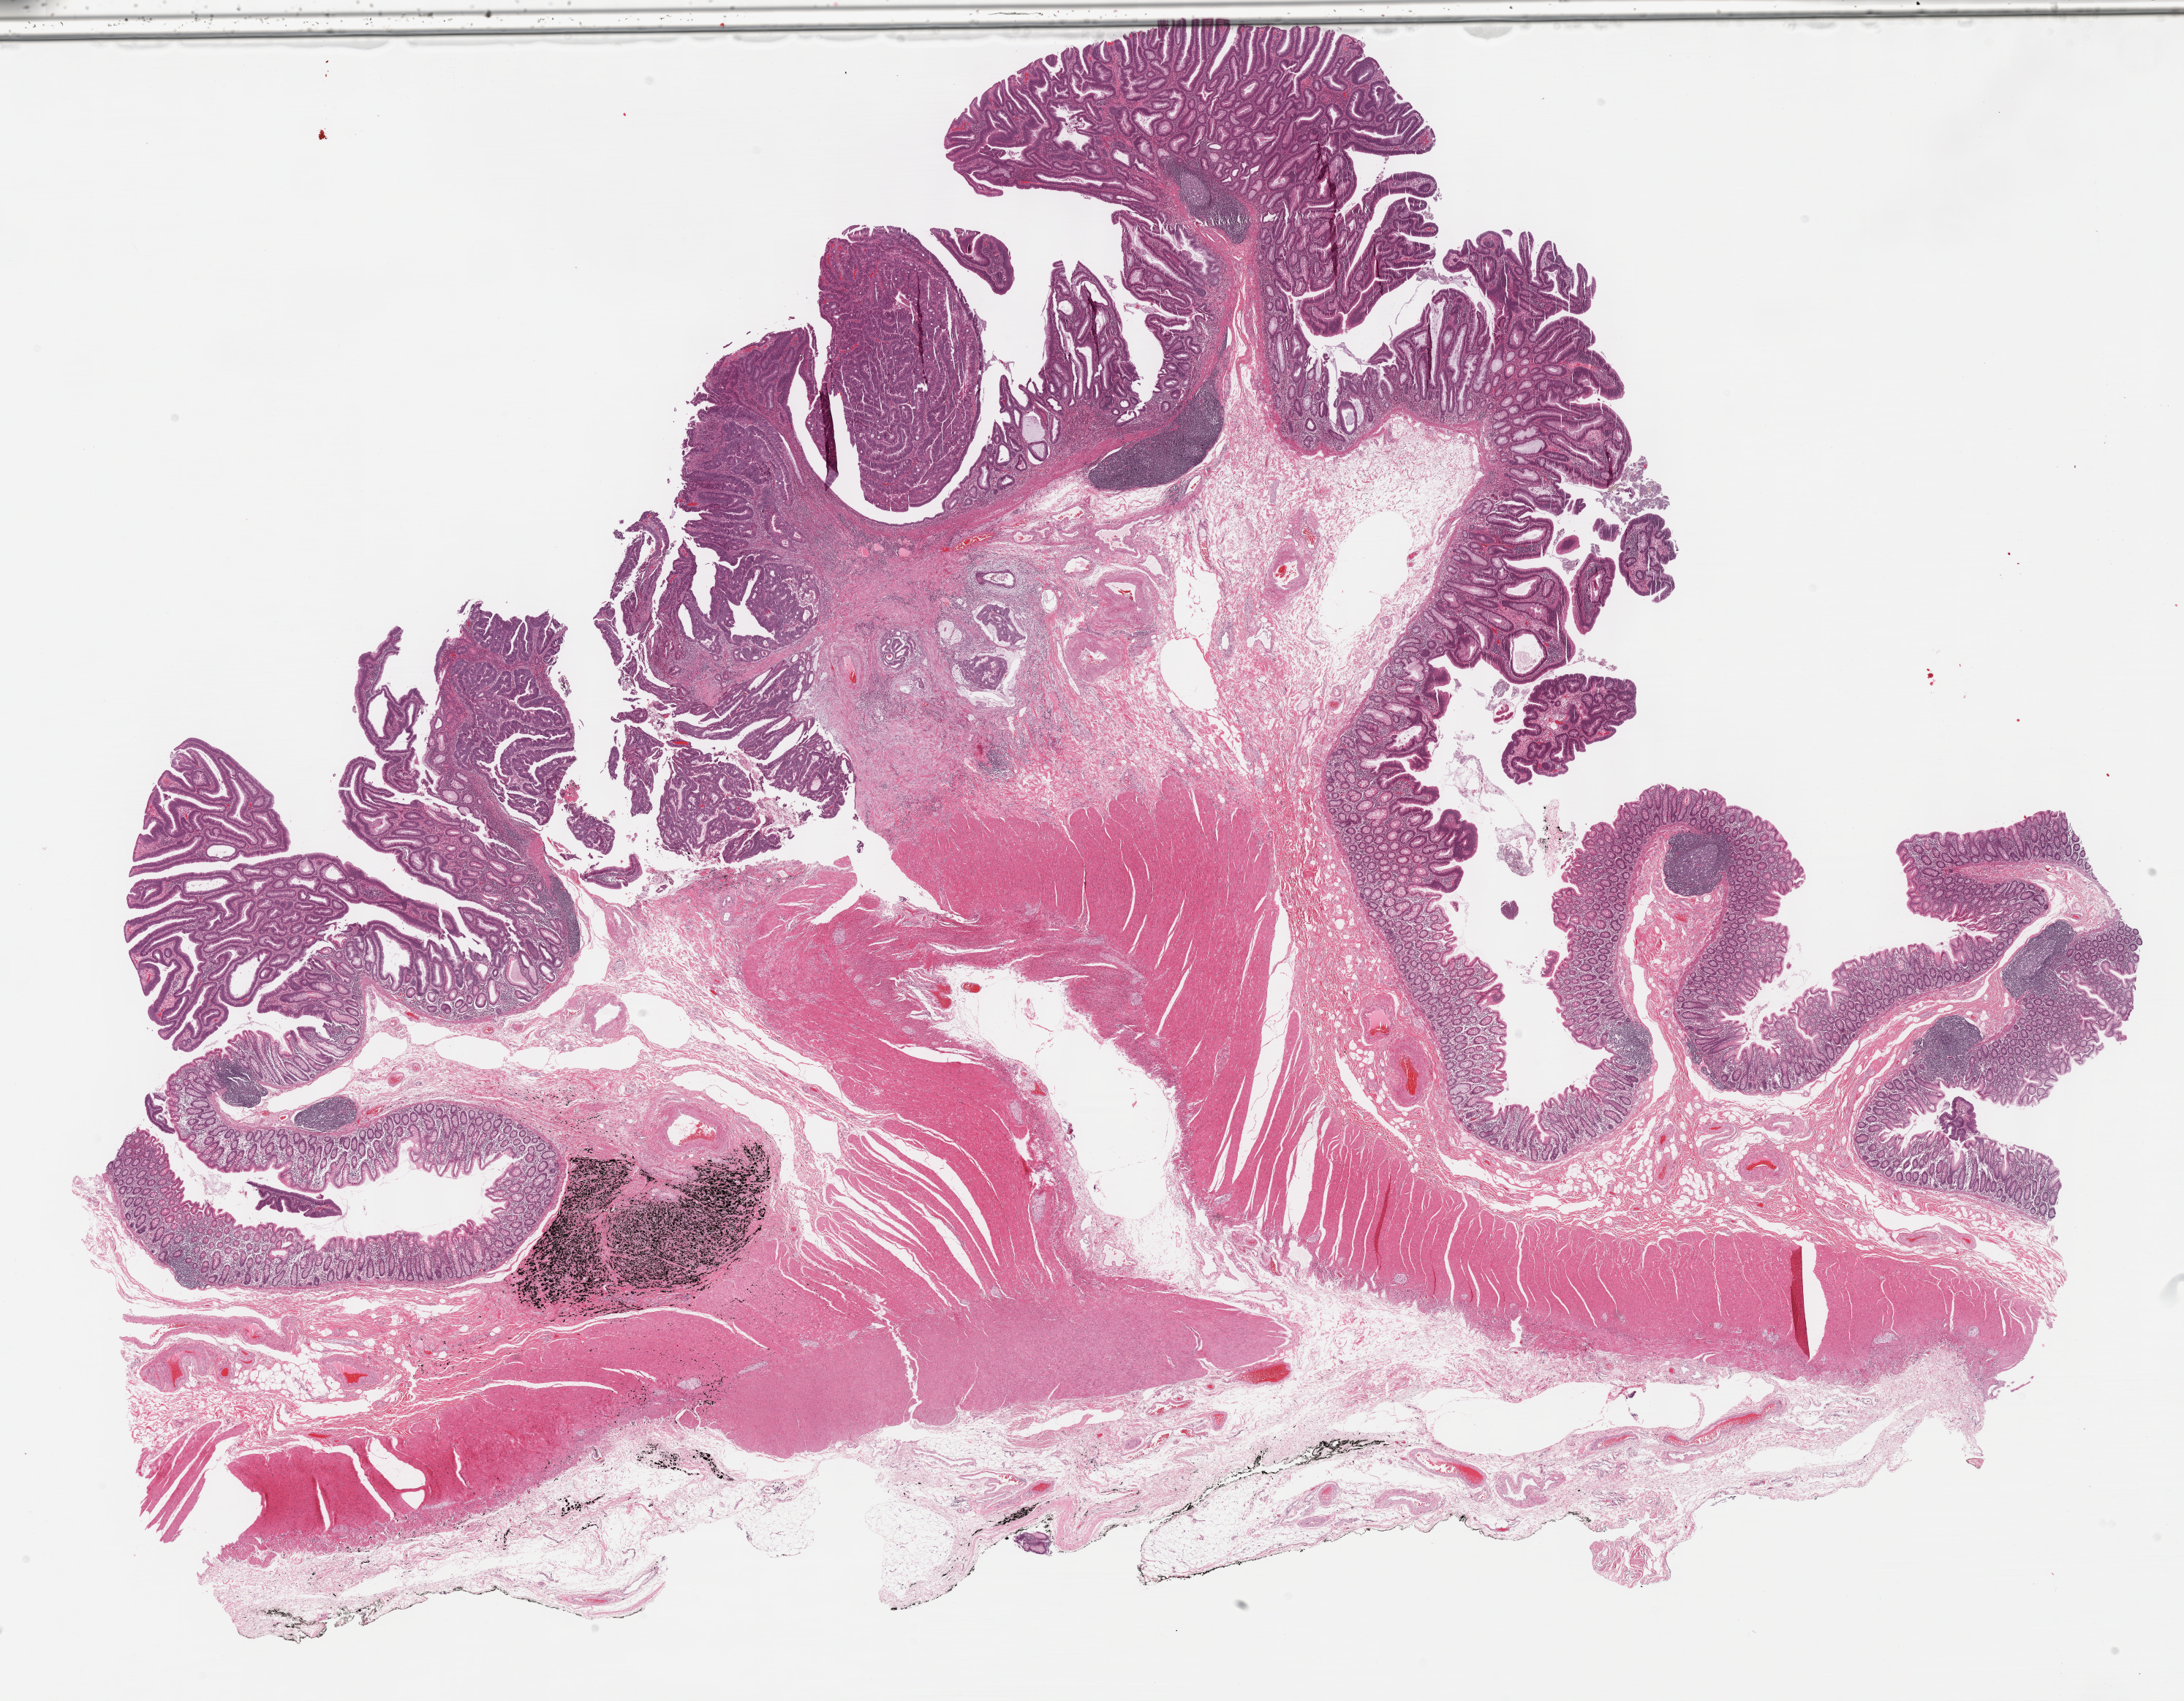
Digitized Hematoxylin and eosin (H&E) stained tissue section (whole slide), shown as a low-resolution overview of the whole scanned area (about 24.2 x 18.8 mm, from a 40x scan); formalin-fixed paraffin-embedded (FFPE) diagnostic section; colon, primary tumour sample. Patient: female, age at initial diagnosis 61 years.
Lymph nodes positive (case pathology): 0 of 28 examined. AJCC pathologic stage: I (7th edition). Pathologic diagnosis: Adenocarcinoma, NOS (cecum).